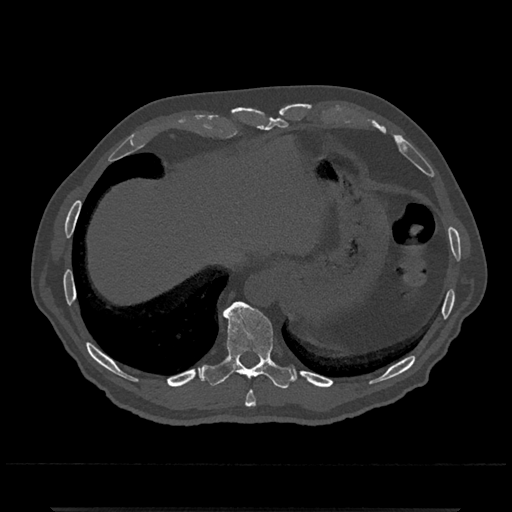
CT including the spine, one axial slice; slice 561 of 797 in the series (ordered by position); reconstruction kernel Br40s/3; bone window (W 1800 / L 400 HU); 0.5 mm slice thickness; 512 × 512 image matrix, field of view 393 × 393 mm. Patient: male, 67 years. Case-level facts recorded for this patient, not image findings: primary cancer: prostate.
Outlined on this slice (semi-automatic segmentation, software-assisted and operator-edited):
- T10 vertebra: bounding box [x1, y1, x2, y2] px = [203, 301, 294, 389]
- T9 vertebra: [245, 391, 256, 407]